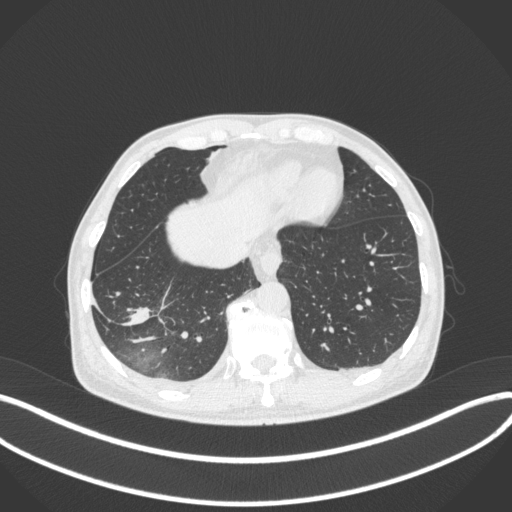
Chest CT, one axial slice; position 89 of 385 along the scan axis; reconstruction kernel B31f; 120 kVp; lung window (W 1500 / L -600 HU); 1 mm slice thickness; 512 × 512 image matrix, field of view 400 × 400 mm. Male patient, age 64 years. Case-level facts recorded for this patient, not image findings: clinical TNM (as recorded): T3 N0 M0.
Outlined on this slice (bounding box drawn by a radiologist):
- lung tumour (recorded histology: adenocarcinoma): bounding box [x1, y1, x2, y2] px = [118, 302, 152, 331]